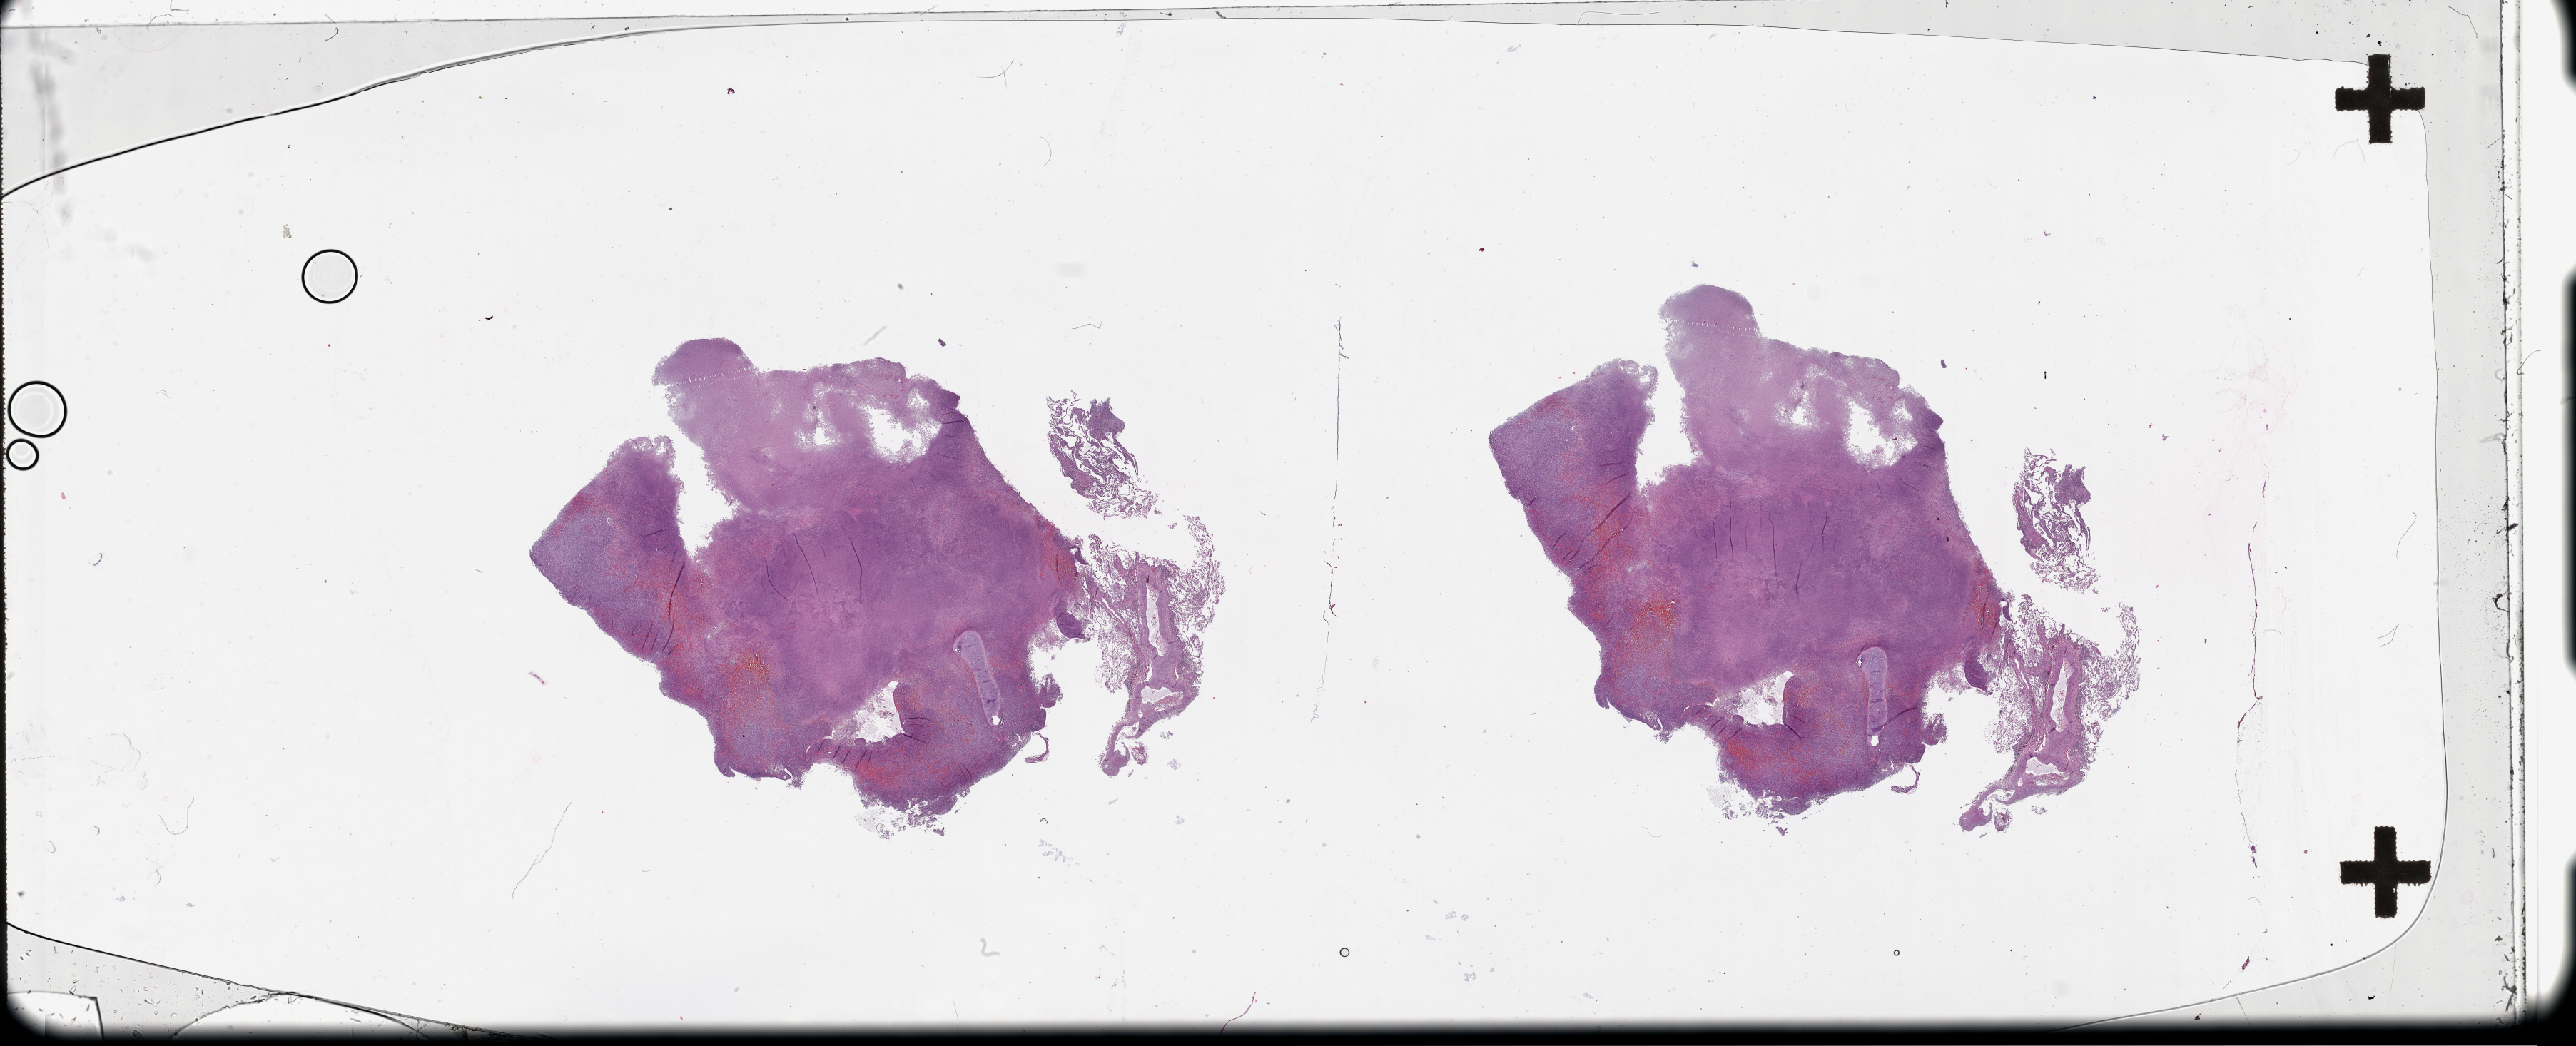
H&E whole-slide image — shown as a low-resolution overview of the whole scanned area (about 58.1 x 23.6 mm, from a 20x scan); tumour tissue sample, lung. 71-year-old male patient.
Patient diagnosis (cohort enrolment): squamous cell carcinoma (lung).